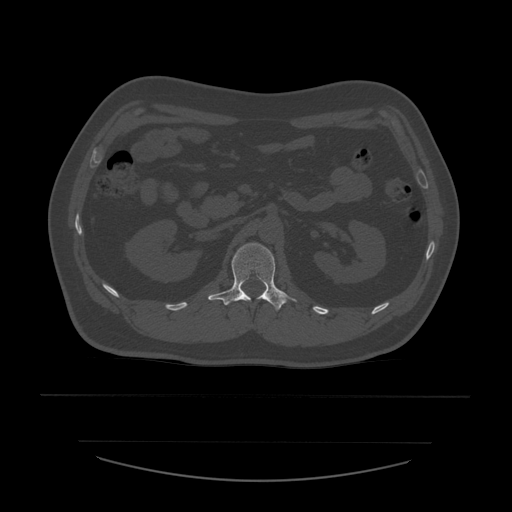
CT including the spine, one axial slice; slice 228 of 532 in the series (ordered by position); reconstruction kernel STANDARD; bone window (W 1800 / L 400 HU); 512 × 512 image matrix. Patient age 44 years. Case-level facts recorded for this patient, not image findings: primary cancer: soft tissue sarcoma.
Annotated regions visible in this slice (semi-automatically segmented with operator editing):
- L1 vertebra: box from (x=208, y=243) to (x=297, y=313) px